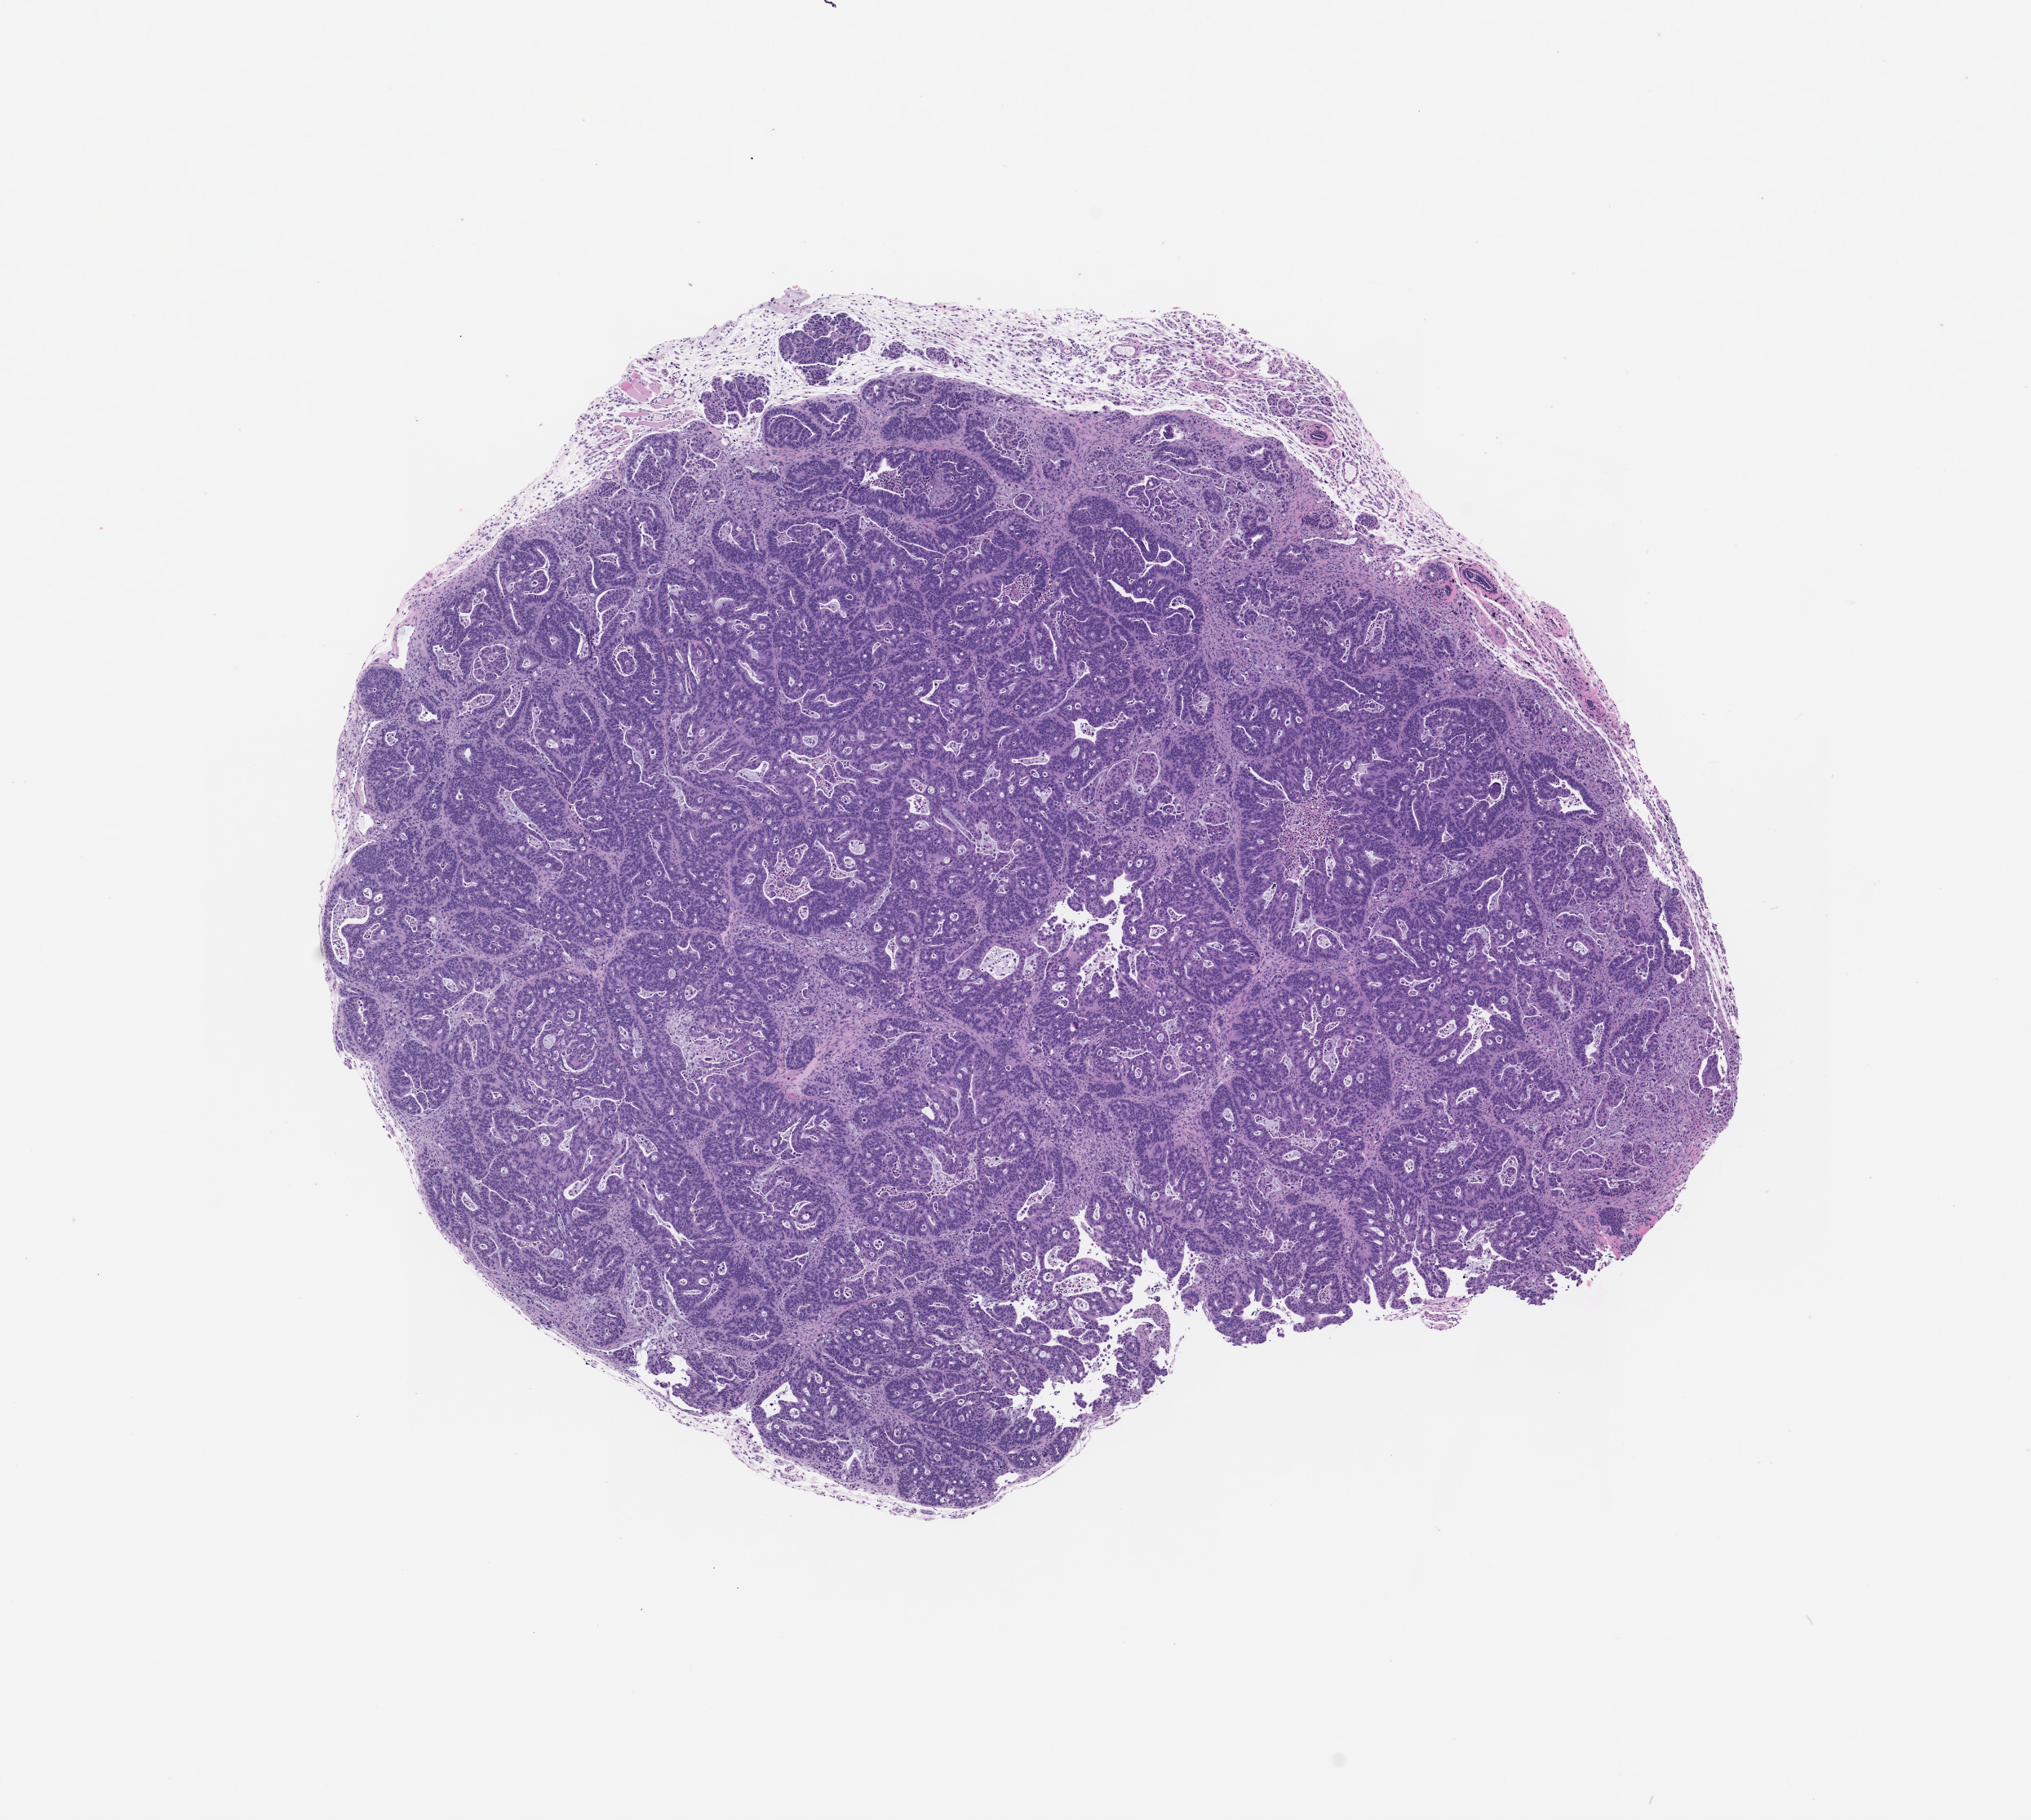
Whole-slide image, H&E: patient-derived xenograft (human tumor grown in a mouse), passage 0 — a low-resolution overview of the entire scanned area, about 10.0 x 8.9 mm; FFPE section; tumor site category: colon.
* originating patient diagnosis: Colon Adenocarcinoma